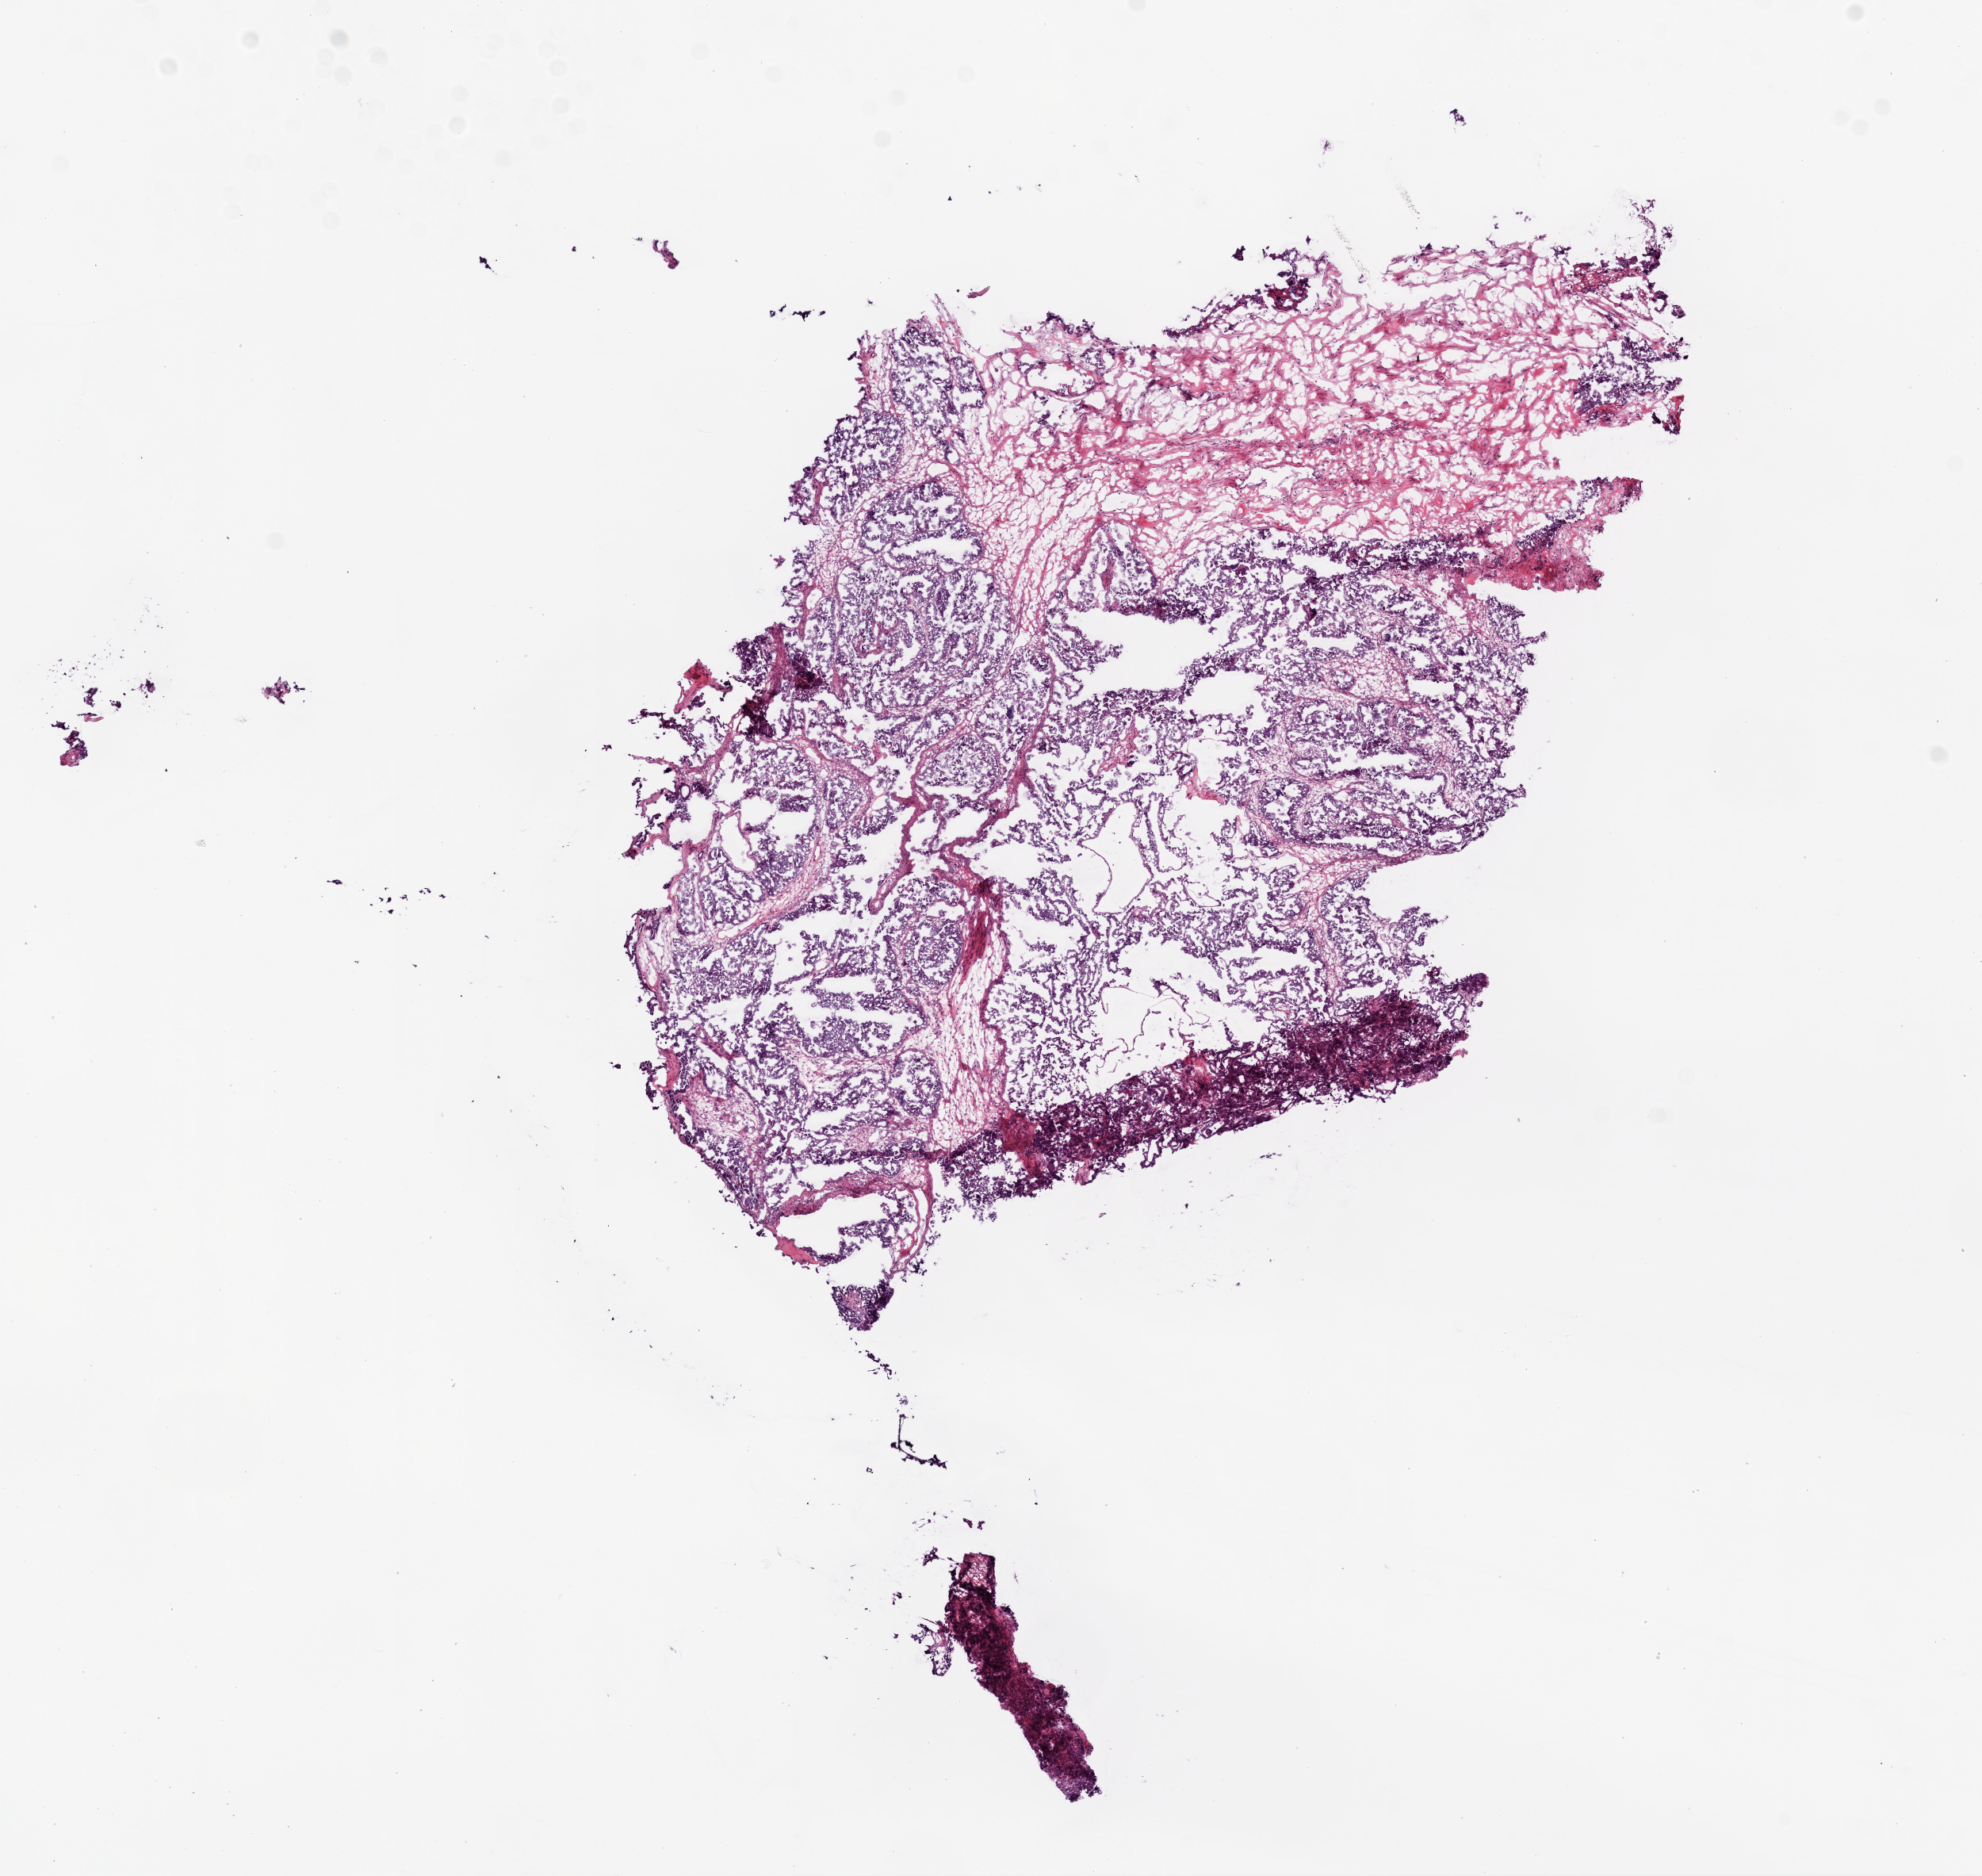
Whole-slide histology image, H&E, whole scanned area (about 10.0 x 9.5 mm) shown as a low-resolution overview; frozen section from the bottom of the tissue portion; primary tumour sample from the ovary. Female patient; age at initial diagnosis 56 years. Histologic grade: G3 (poorly differentiated). Slide review estimates, as recorded: tumour cells 60%, tumour nuclei 81%, normal cells 30%, stromal cells 0%, necrosis 10%.
Laterality: bilateral. FIGO stage: IIIC. Pathologic diagnosis: Serous cystadenocarcinoma, NOS.